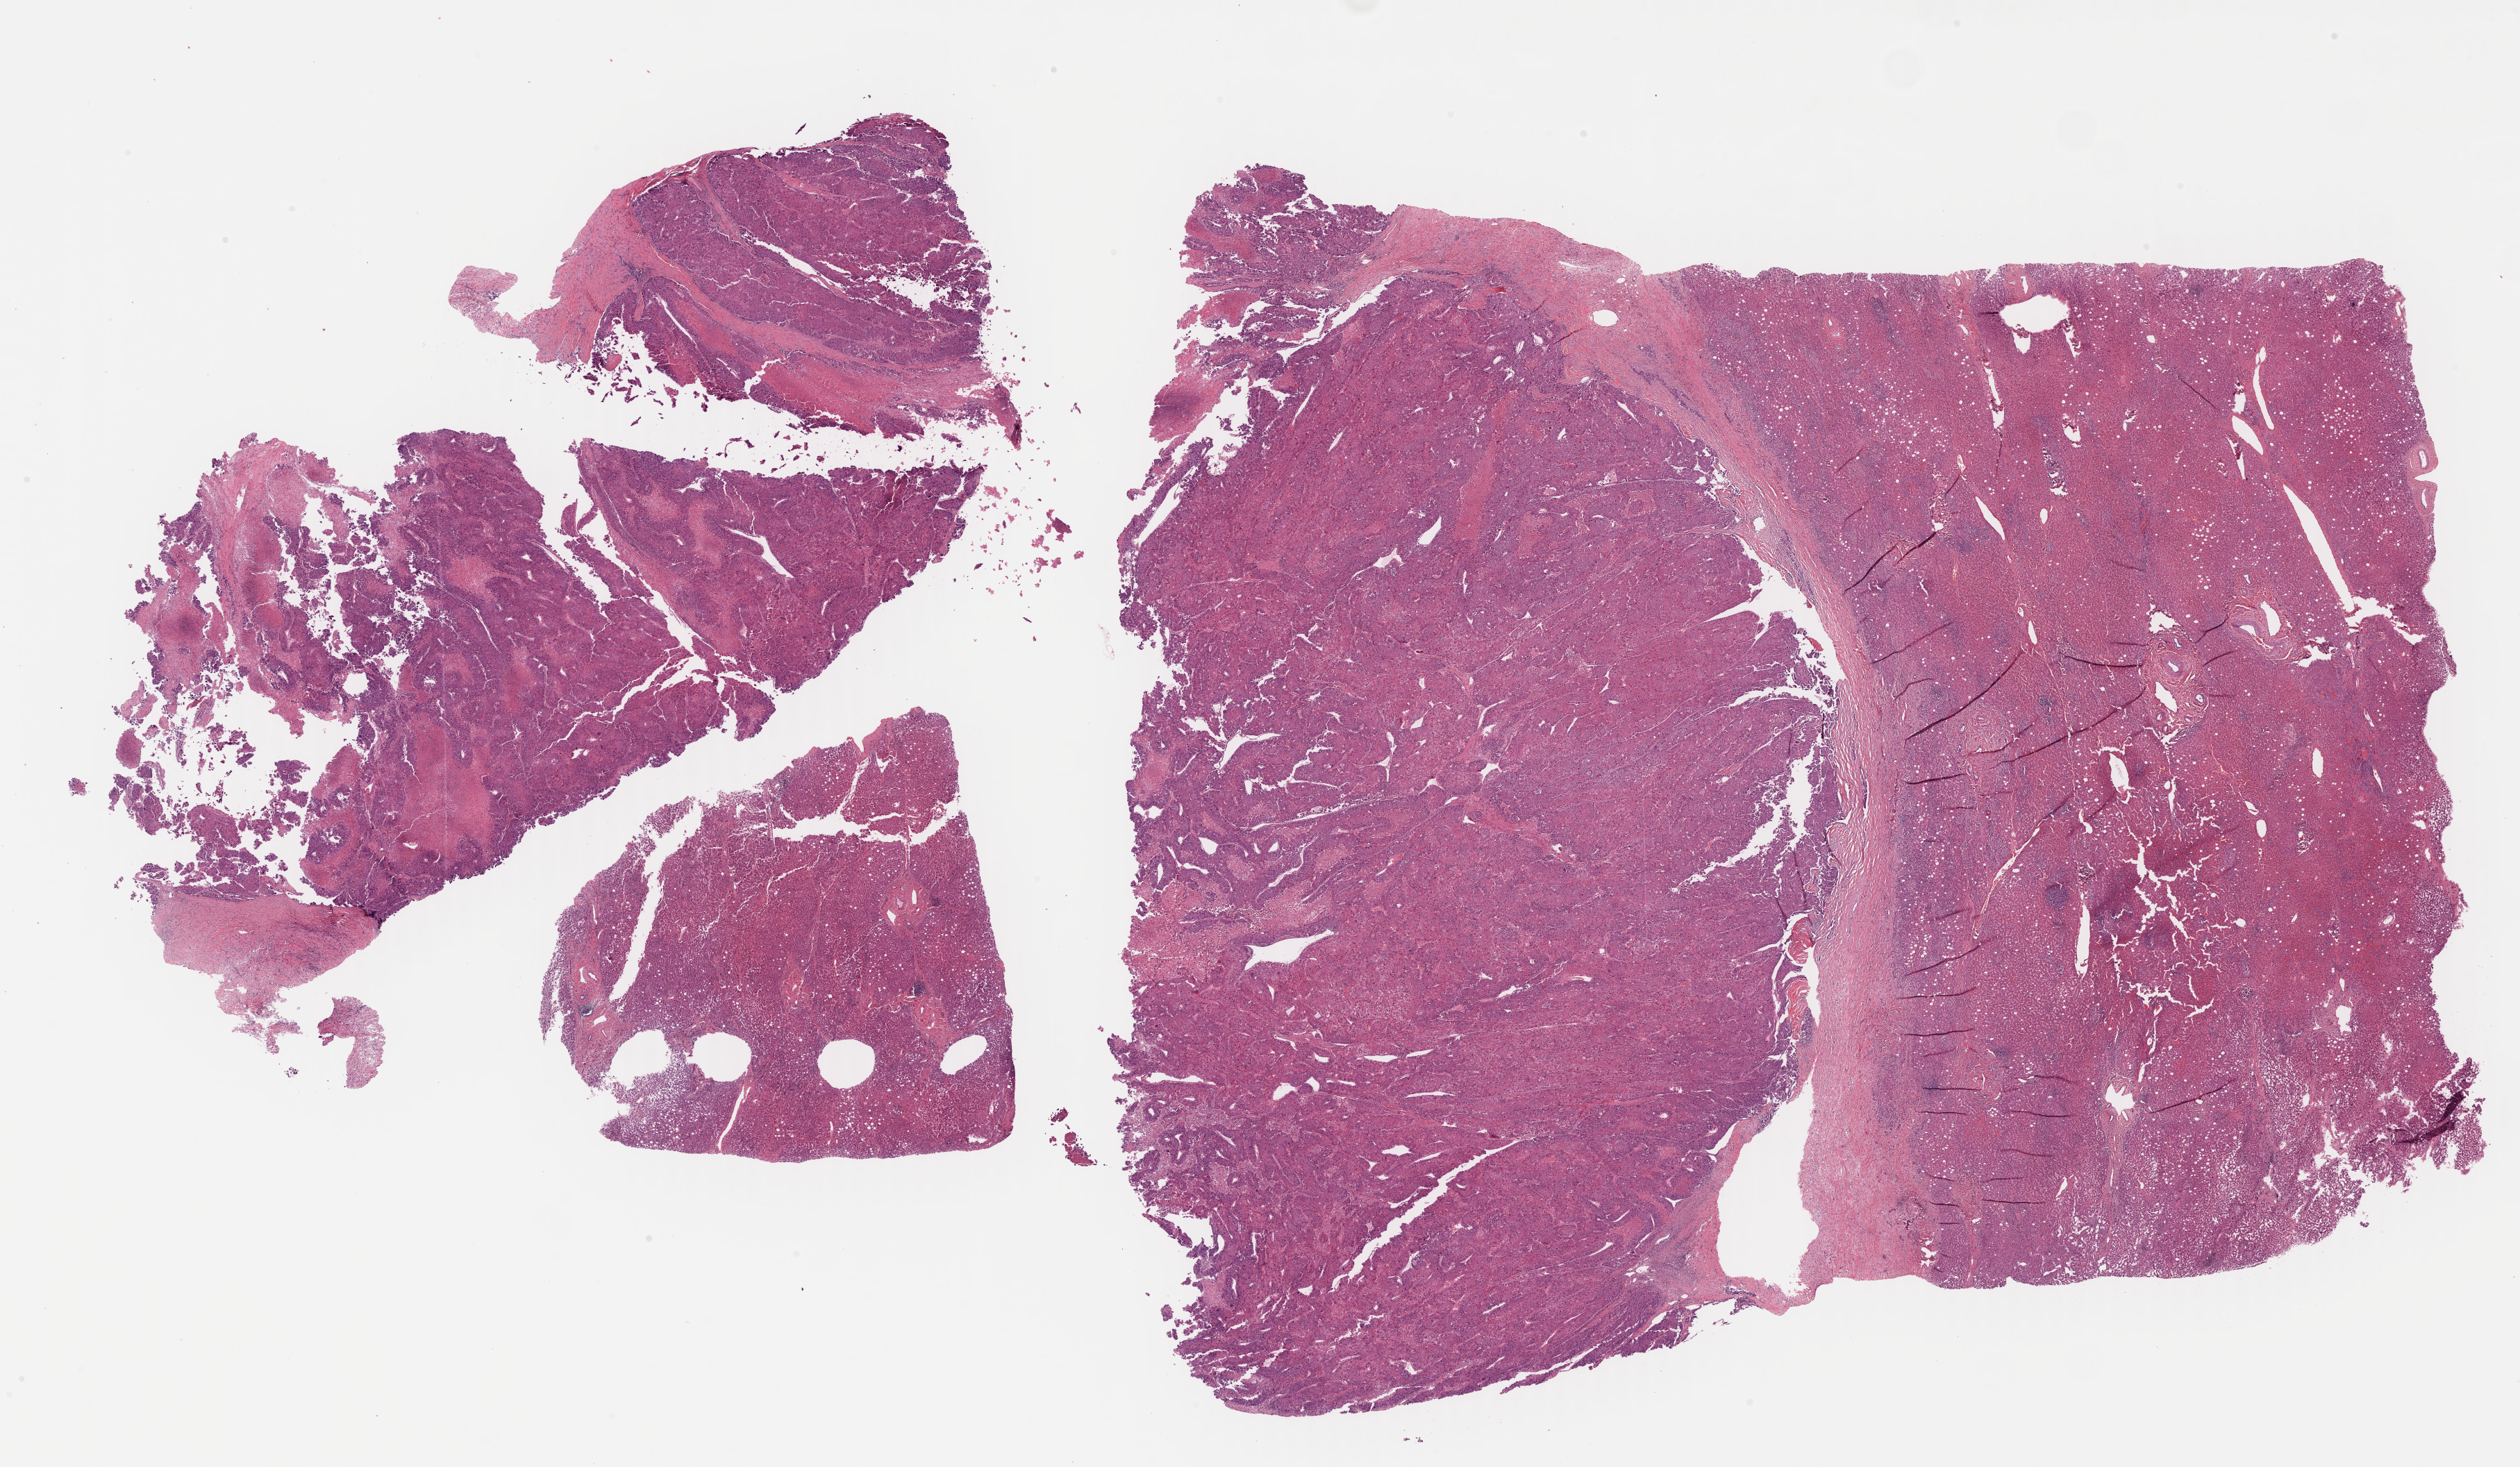
Whole-slide histology image, H&E-stained, a low-resolution overview of the entire scanned area, about 29.4 x 17.1 mm, FFPE section, liver, primary tumour sample. Male, age 60 years at initial diagnosis. Histologic grade: G3 (poorly differentiated).
• TNM: T2 N0 M0
• AJCC pathologic stage: II
• diagnosis: Hepatocellular carcinoma, NOS